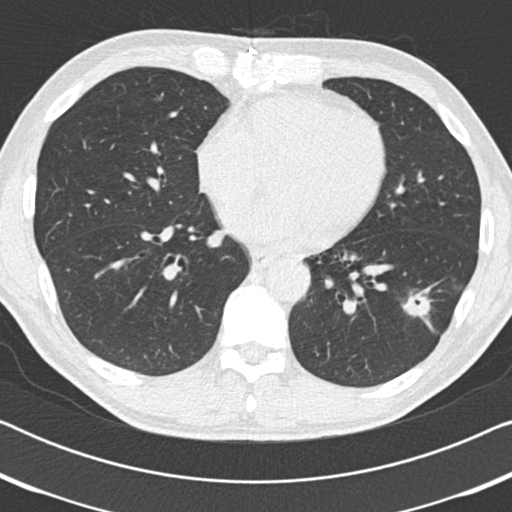
Low-dose screening chest CT, one axial slice; position 77 of 186 along the scan axis; reconstruction kernel B30f; 120 kVp; lung window (W 1500 / L -600 HU); 512 × 512 image matrix, field of view 330 × 330 mm.
Structures marked on this image (expert manual segmentation):
- lesion 1 (tumor, lower lobe of left lung): box from (x=403, y=292) to (x=431, y=319) px